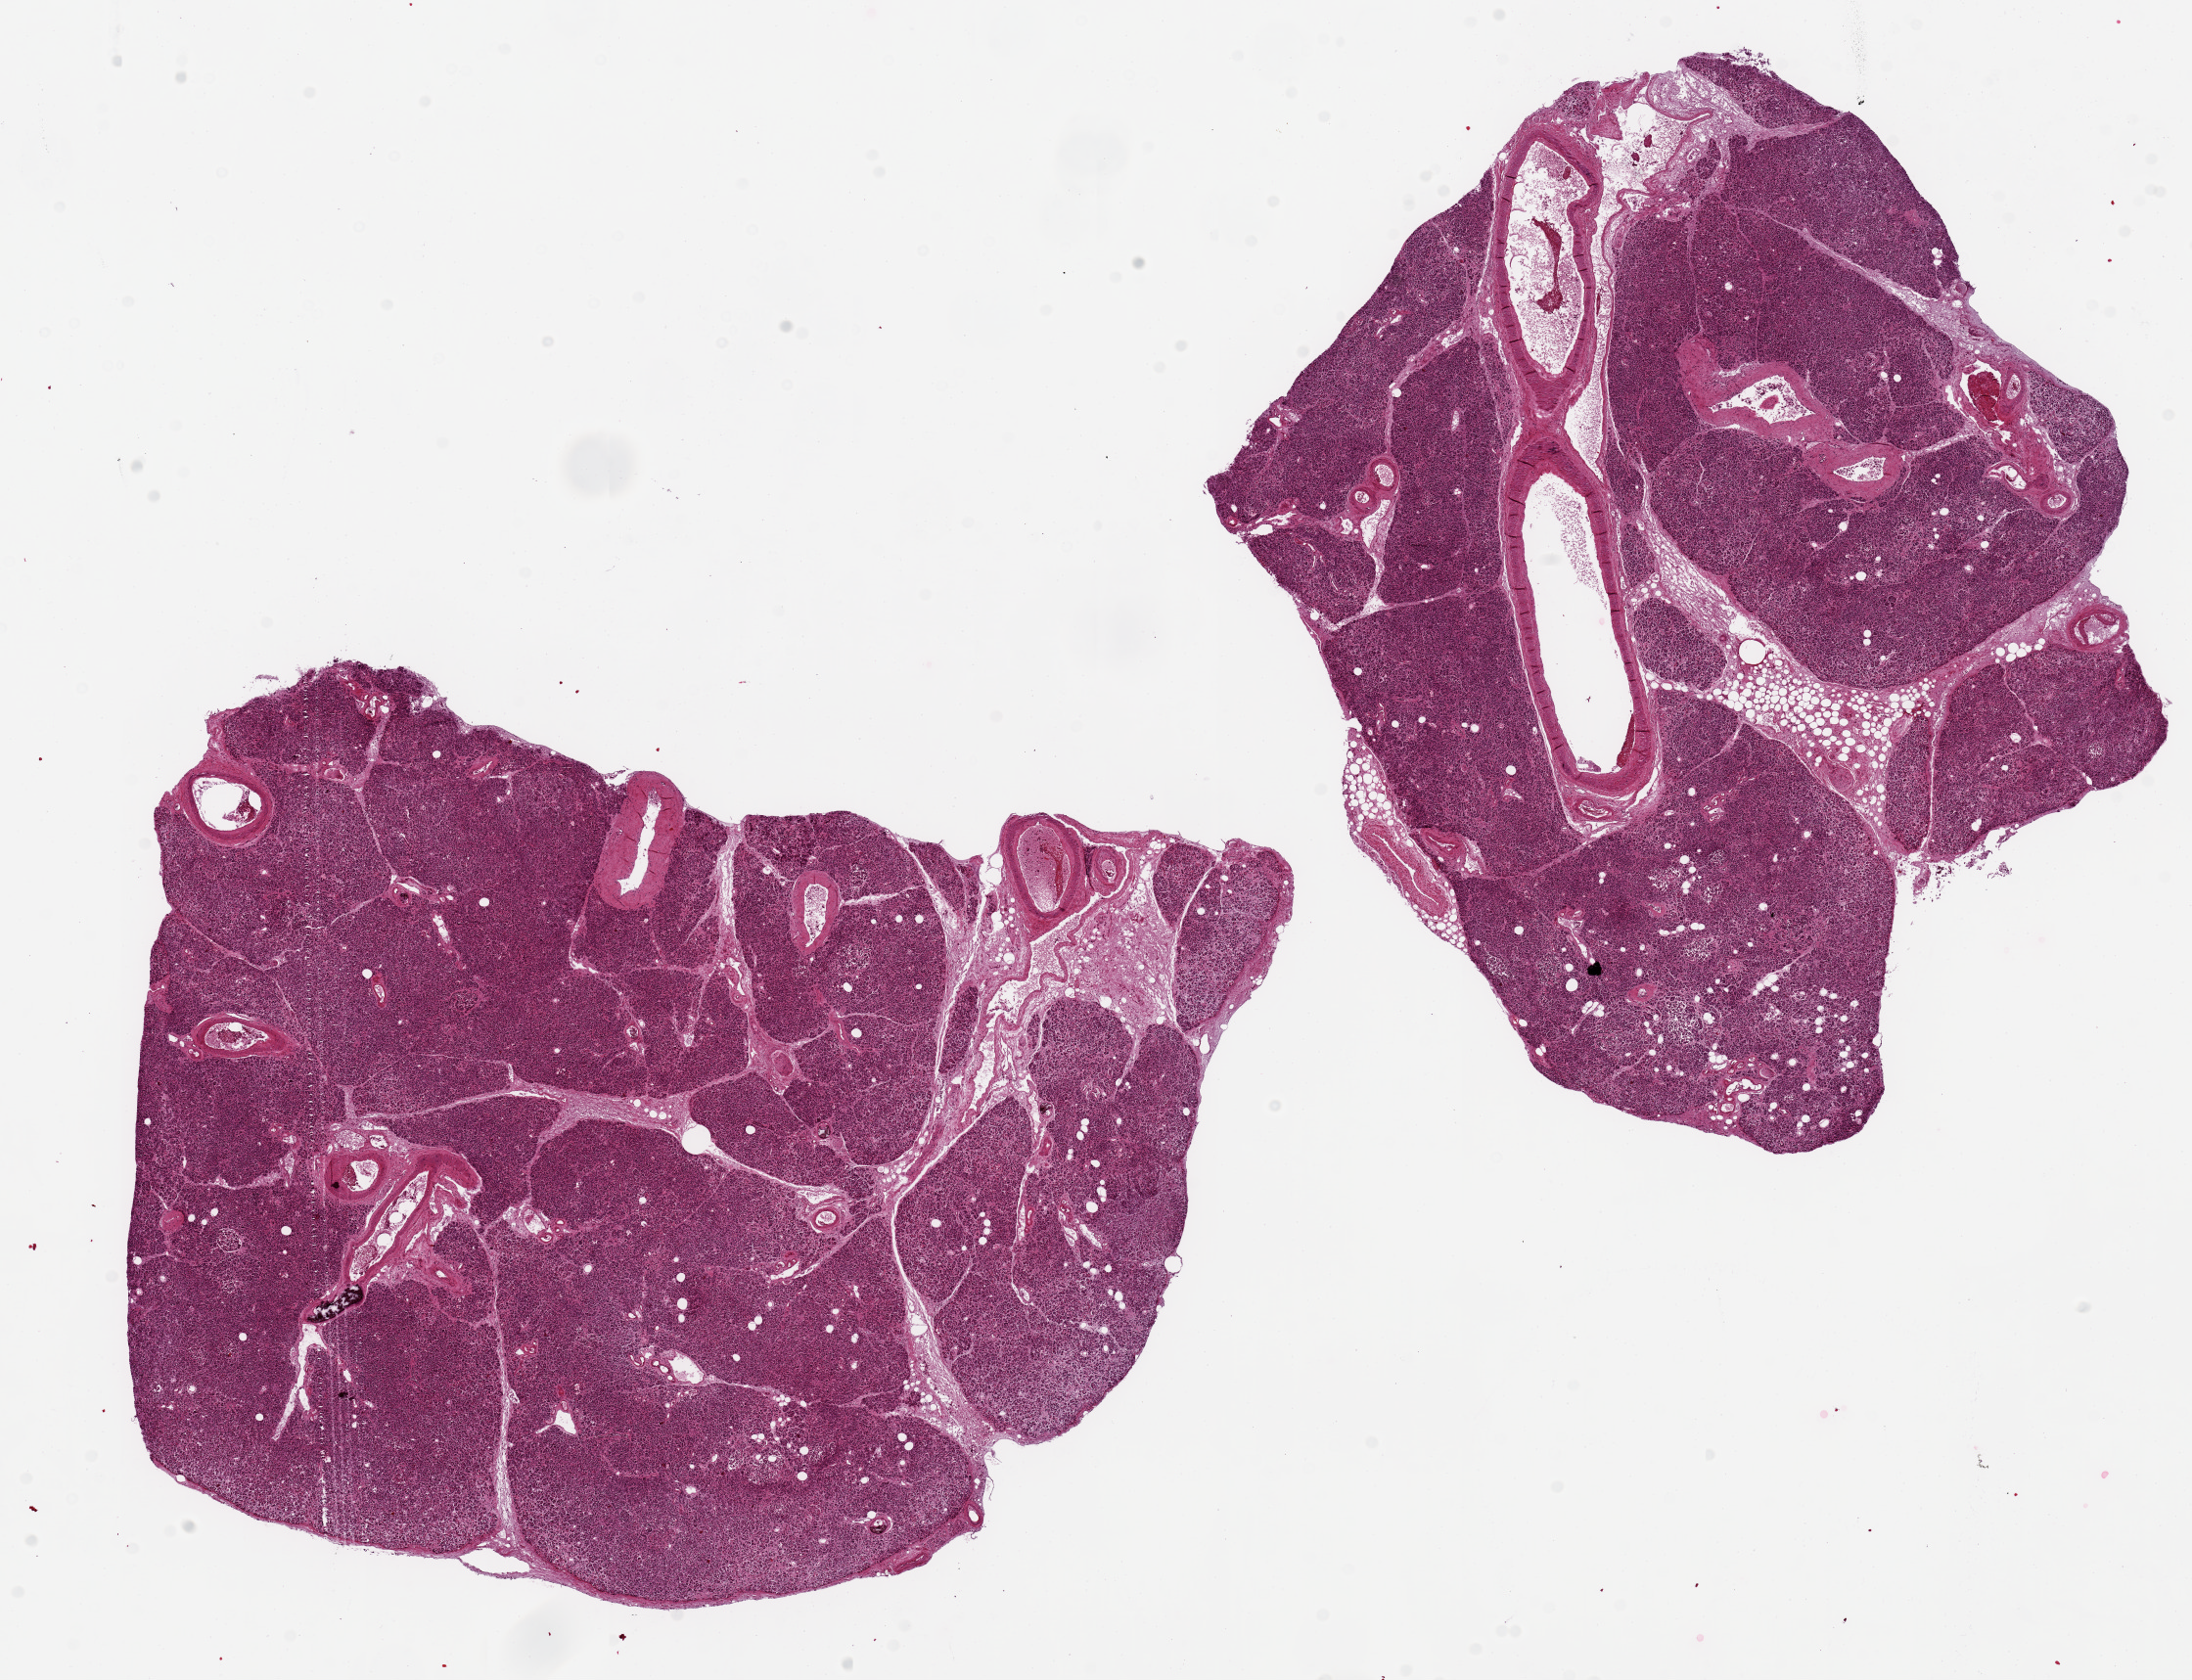
Digitized hematoxylin and eosin (H&E)-stained section, shown as a low-resolution overview of the whole scanned area (about 17.7 x 13.6 mm, acquisition: 20x scan); PAXgene-fixed paraffin-embedded (PFPE) section; target tissue: pancreas; donor tissue sample. Donor sex: male.
Reviewer comment on this tissue sample: 2 pieces, 9x7 & 8x7mm; Several calcified small arteries. 10% internal adipose in one piece.